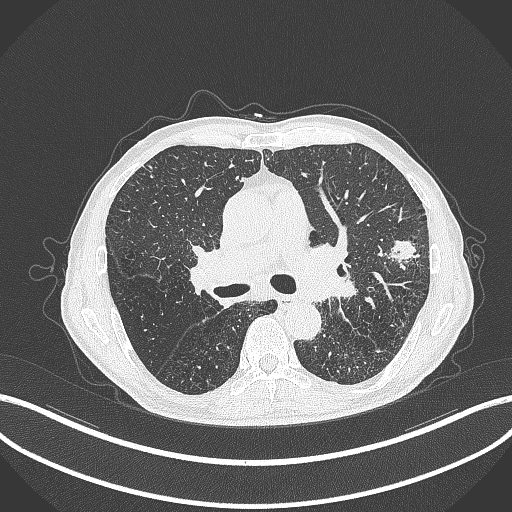
Chest CT, one axial slice; slice 254 of 463 in the series (ordered by position); 120 kVp; lung window (W 1500 / L -600 HU); 1 mm slice thickness; 512 × 512 image matrix, field of view 400 × 400 mm. Patient: male, 74 years. Case-level facts recorded for this patient, not image findings: clinical TNM (as recorded): T2a N1 M0.
Structures marked on this image (bounding box drawn by a radiologist):
- lung tumour (recorded histology: adenocarcinoma): bounding box (x1, y1, x2, y2) in pixels: (387, 235, 424, 268)